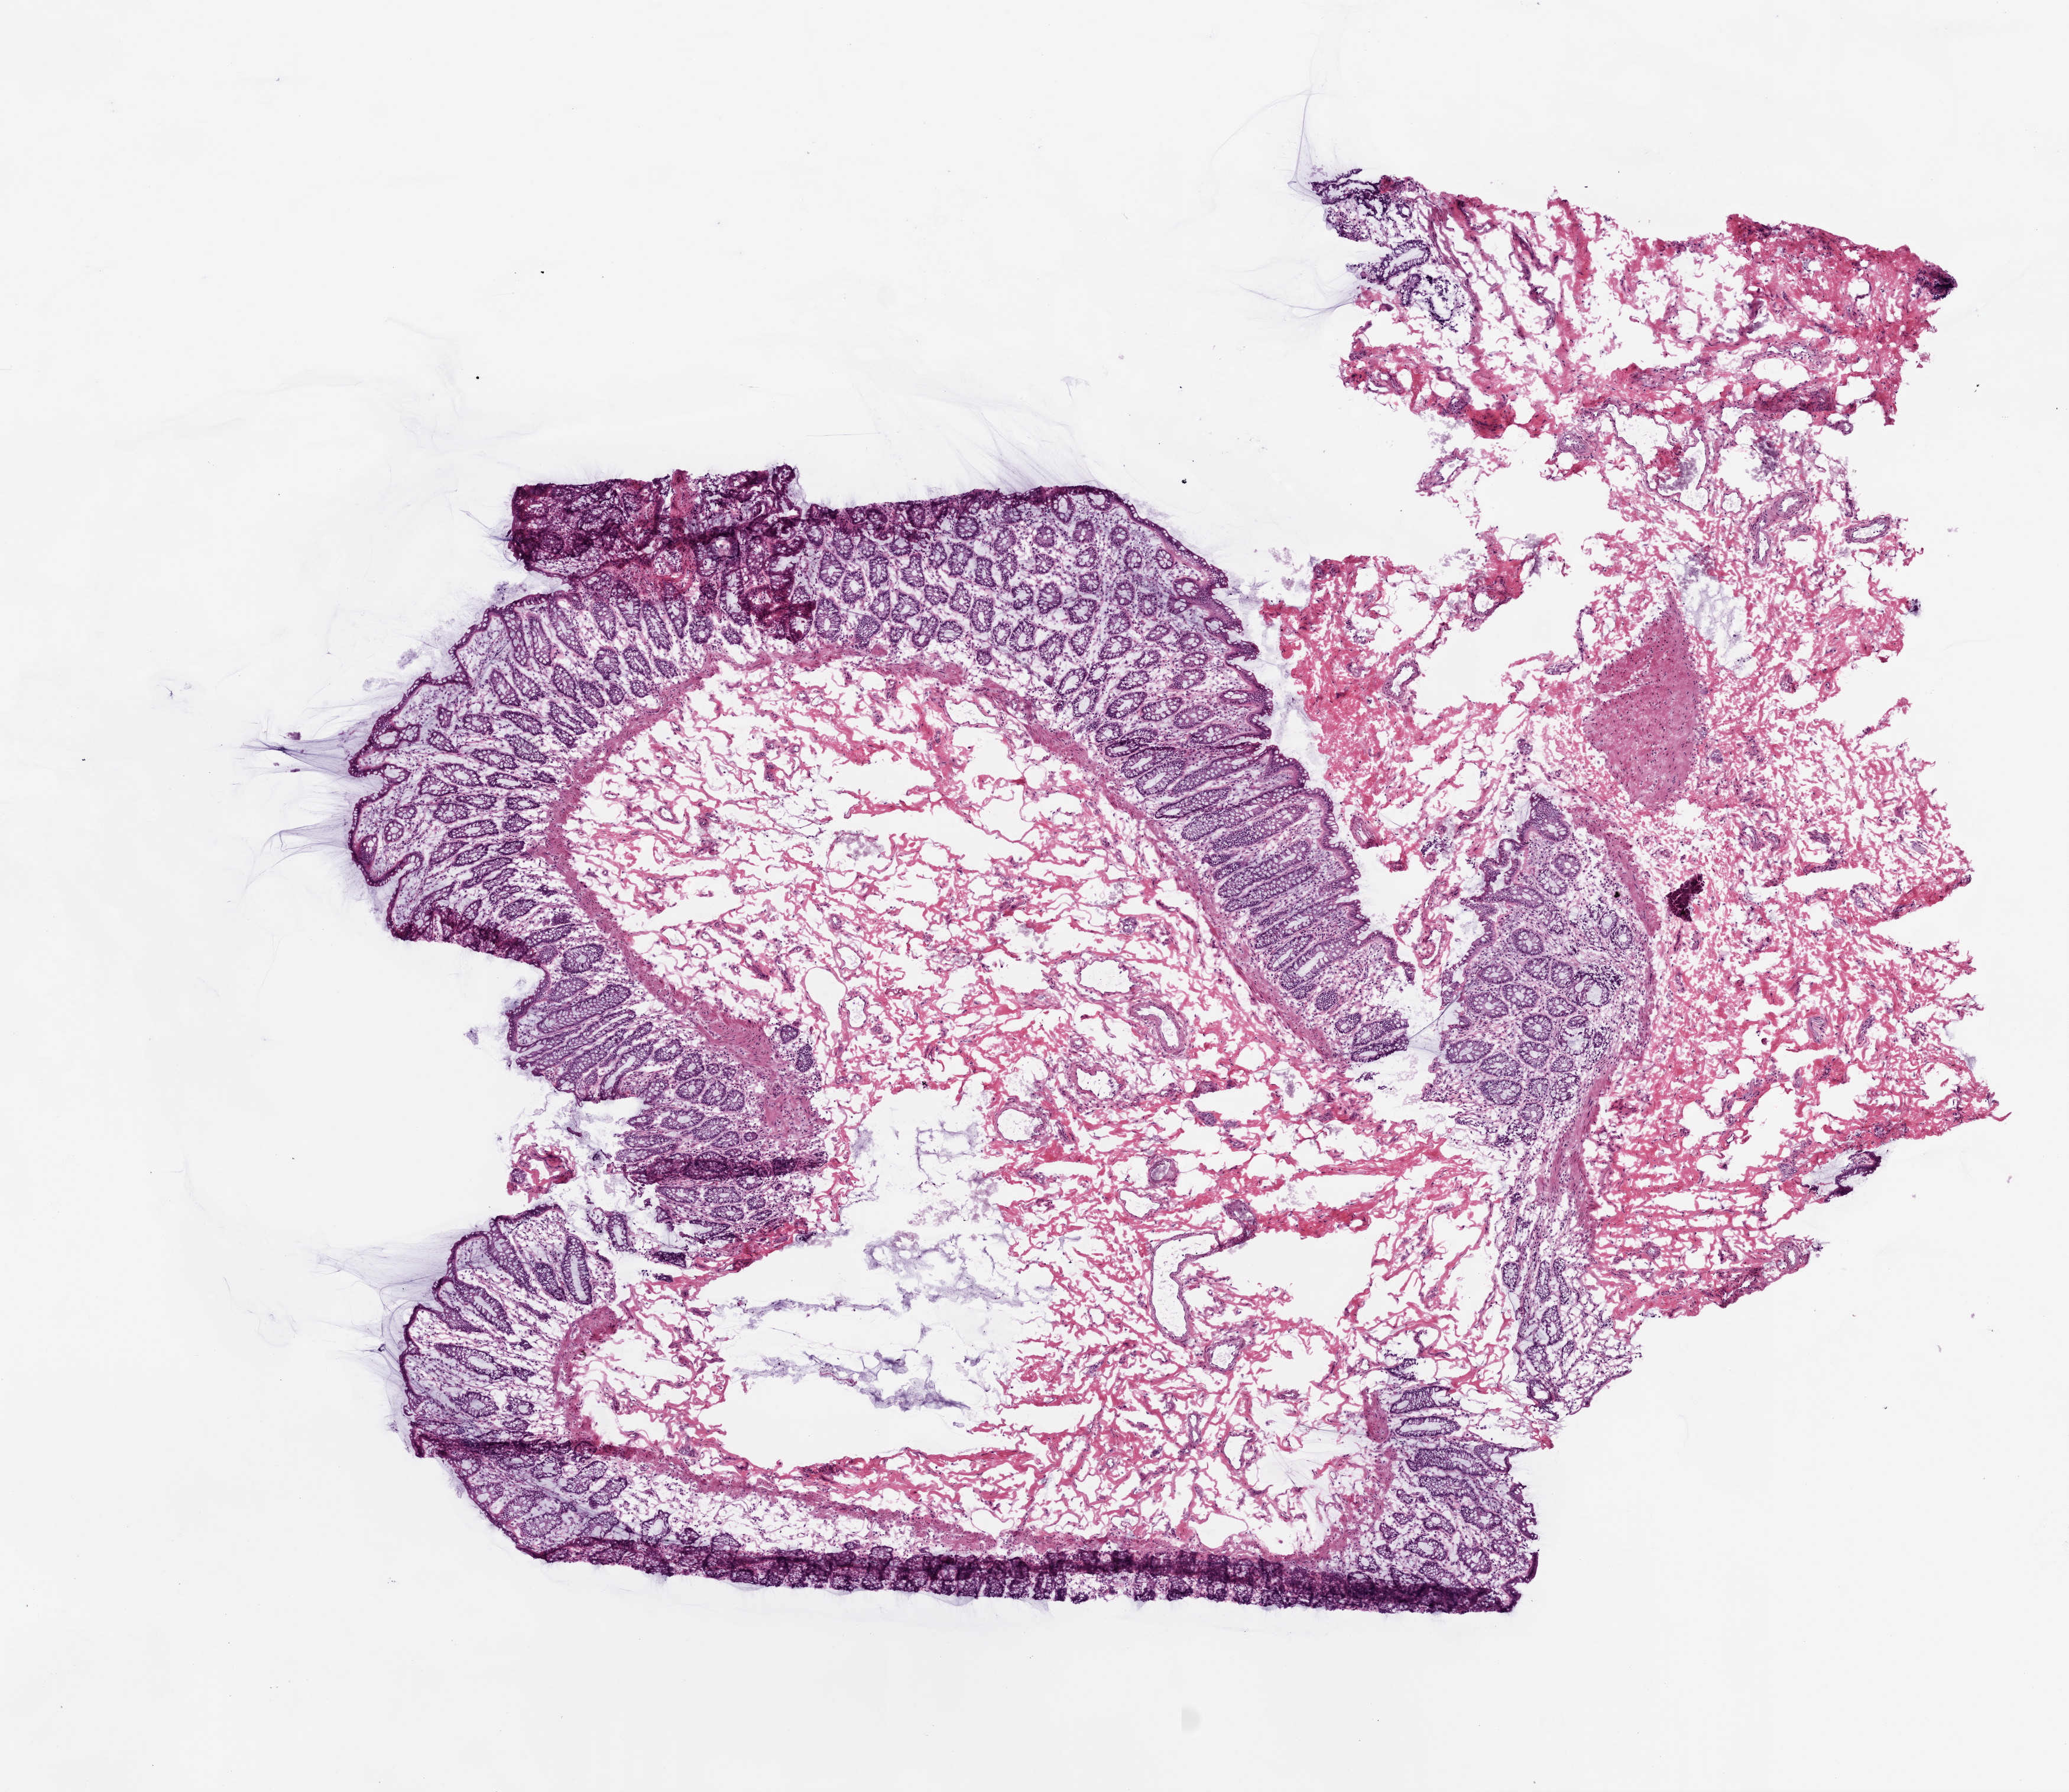
Whole-slide histology image, H&E, whole scanned area (about 7.0 x 6.1 mm, acquisition: 20x scan) shown as a low-resolution overview; frozen section; colon, solid tissue normal (non-tumour tissue) sample. Female, age 78 years at initial diagnosis.
This section: solid tissue normal sample (biorepository sample class). Patient diagnosis: Adenocarcinoma, NOS (sigmoid colon).